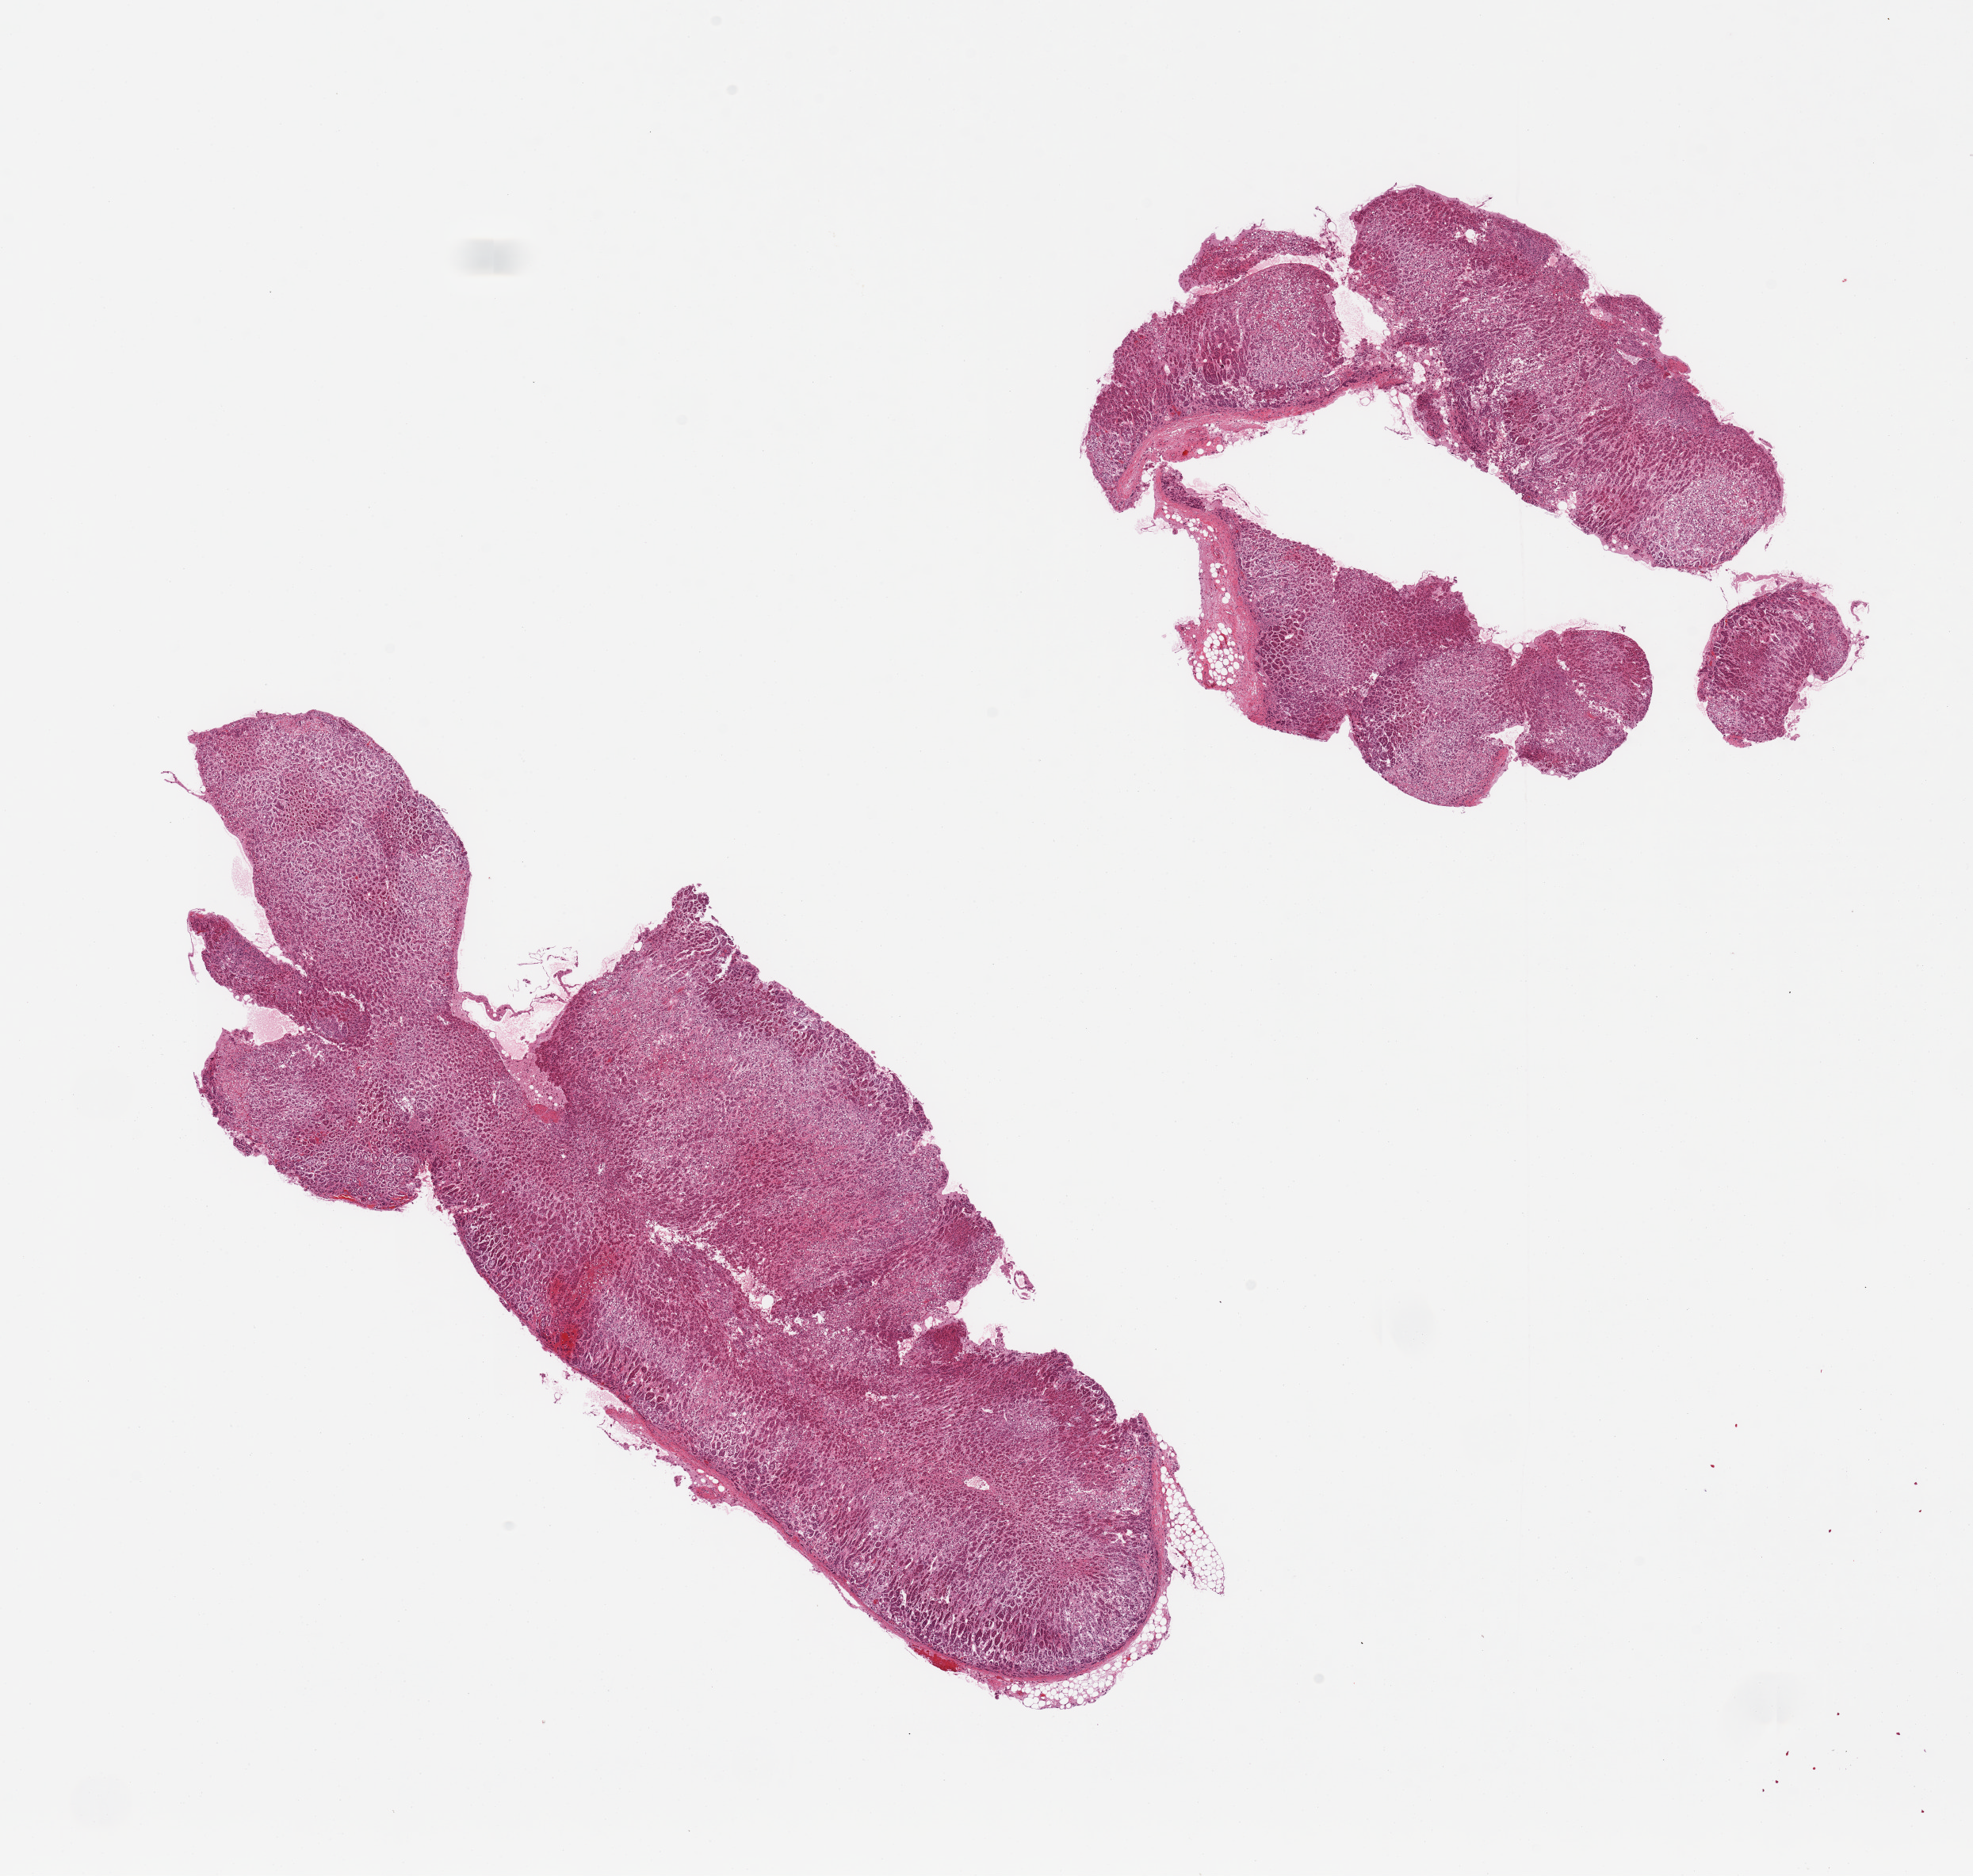
Whole-slide image, haematoxylin and eosin stain, brightfield, a low-resolution overview of the entire scanned area, about 19.7 x 18.7 mm, PAXgene-fixed paraffin-embedded (PFPE) section, target tissue: adrenal gland, donor tissue sample. Donor: female.
- pathologist's review note for this sample: 2 pieces, 1 fragmented, all cortex, minimal fat